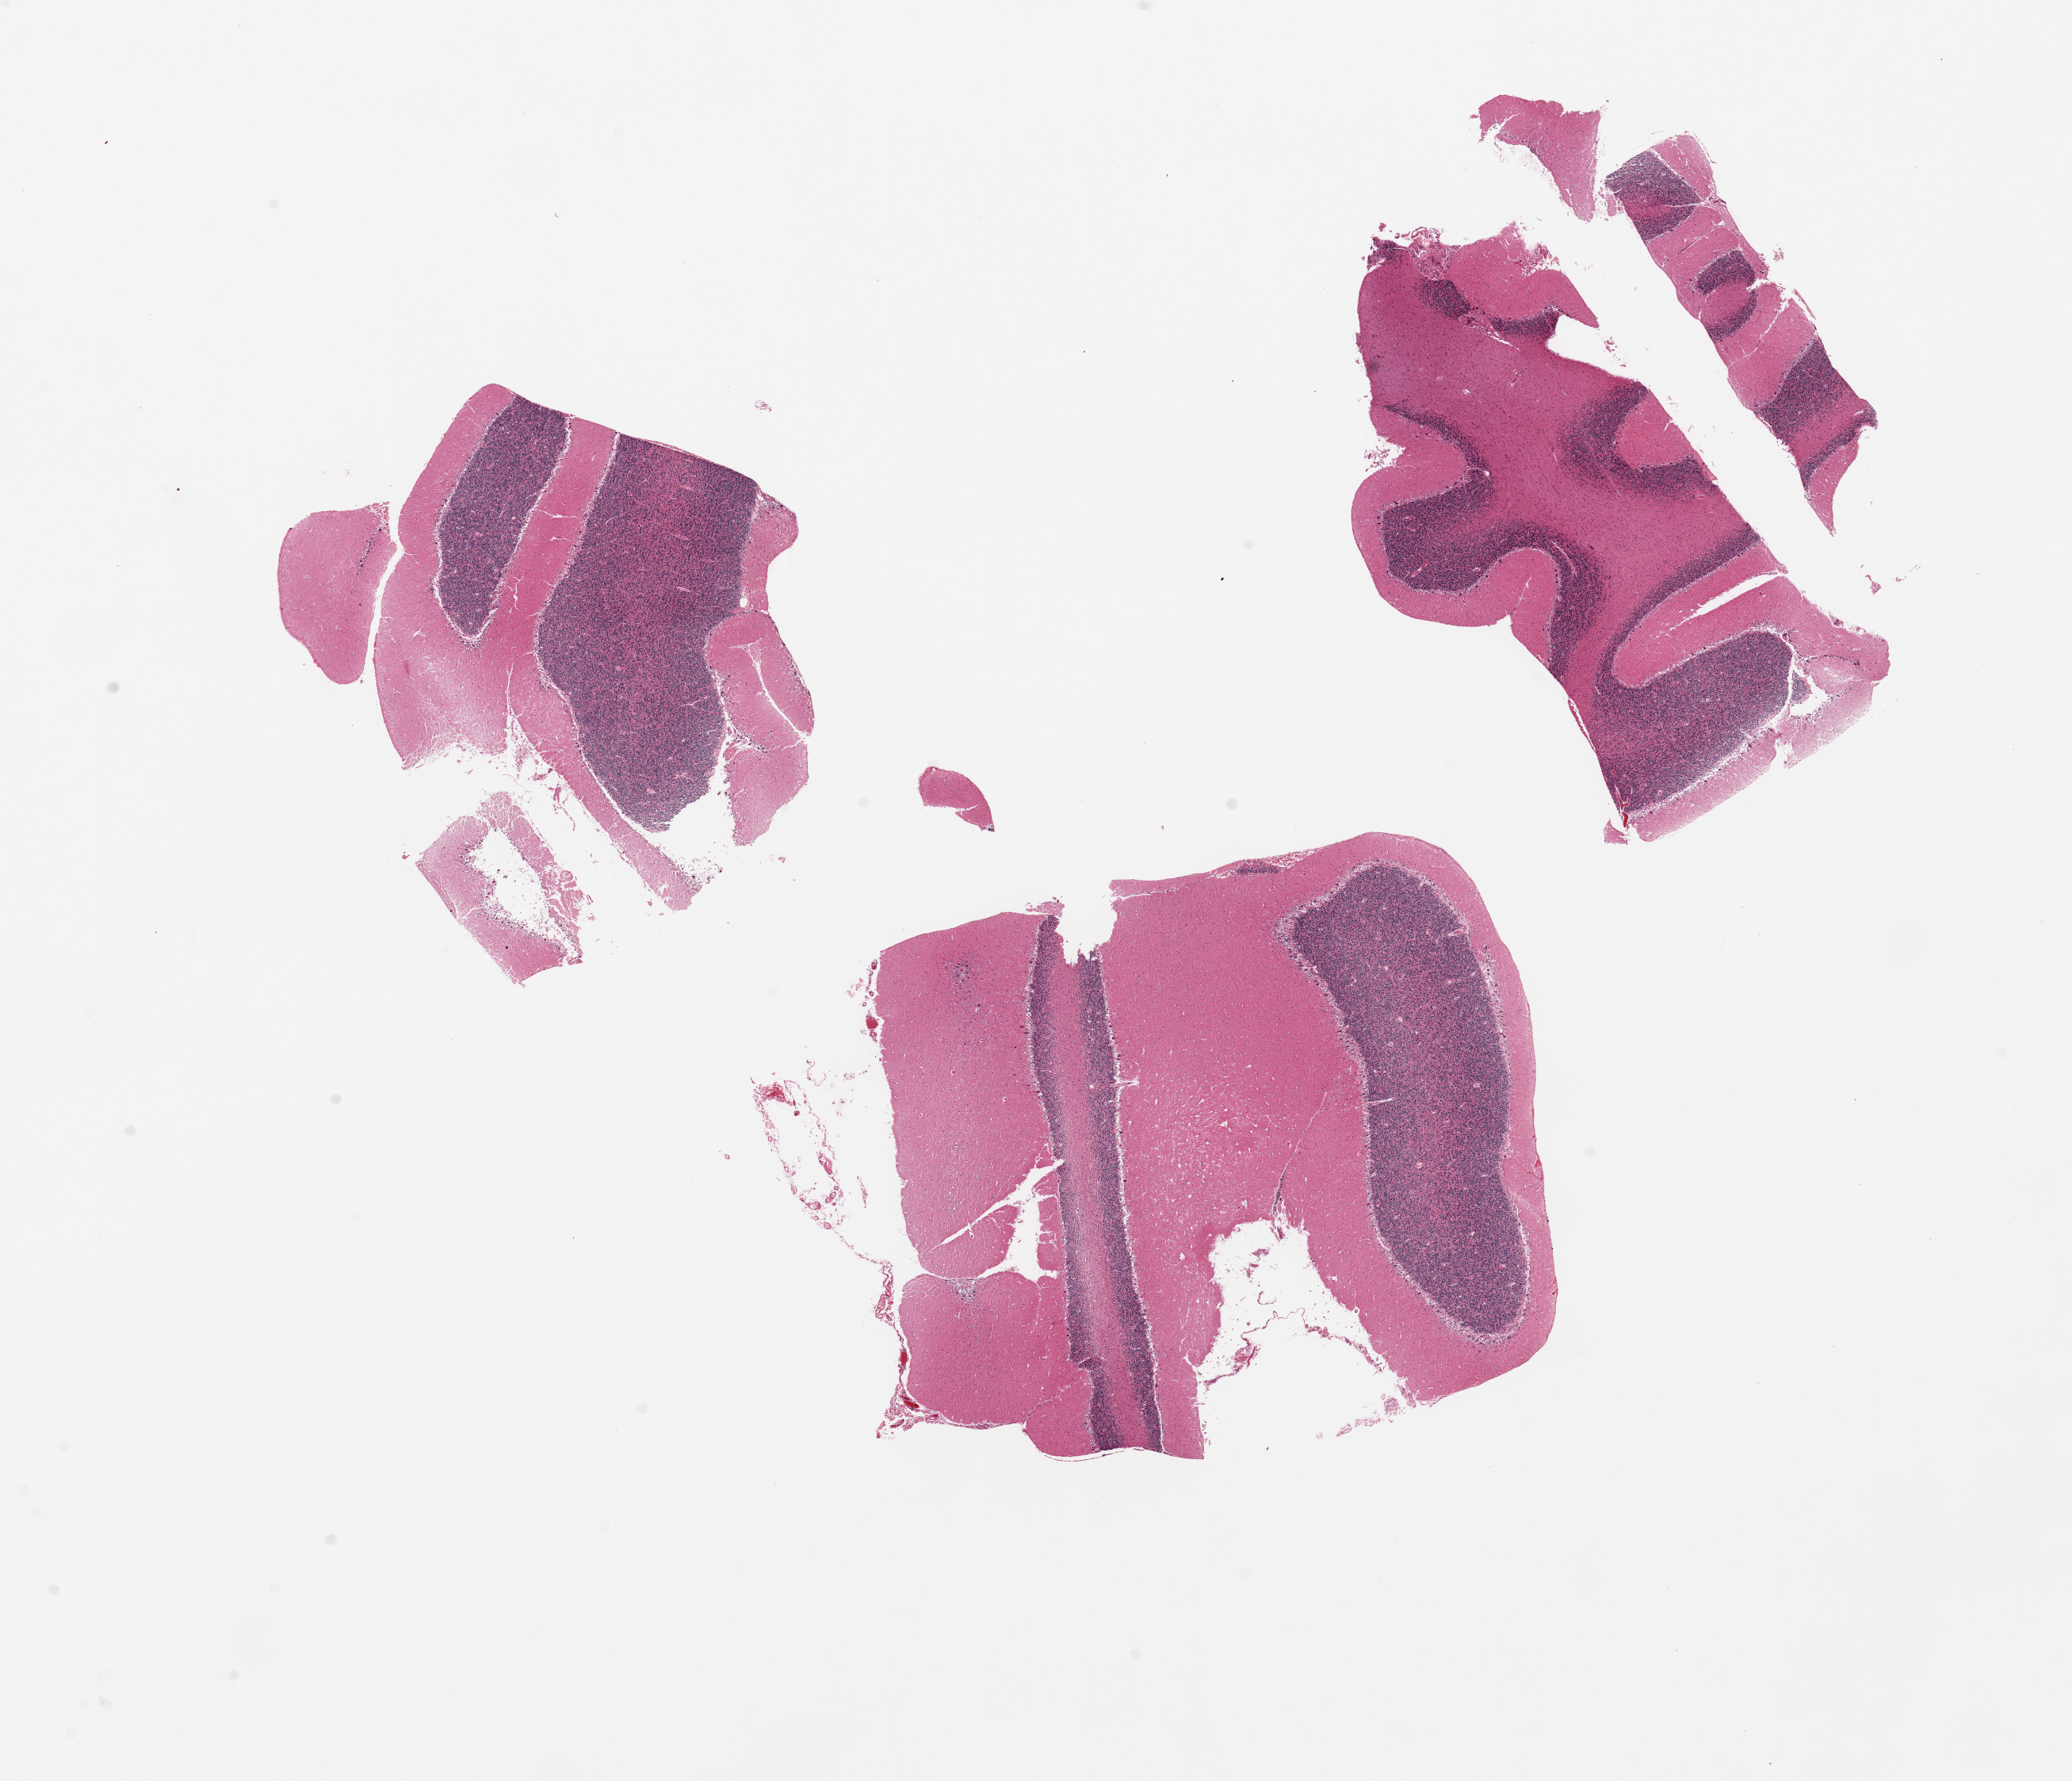
H&E whole-slide image, brightfield — low-resolution overview of the scanned area, about 20.7 x 17.8 mm (acquisition: 20x scan); PAXgene-fixed paraffin-embedded (PFPE) section; target tissue: cerebellum; tissue donor sample. Donor sex: male.
Pathologist's review note for this sample: 3 pieces; fragmented.